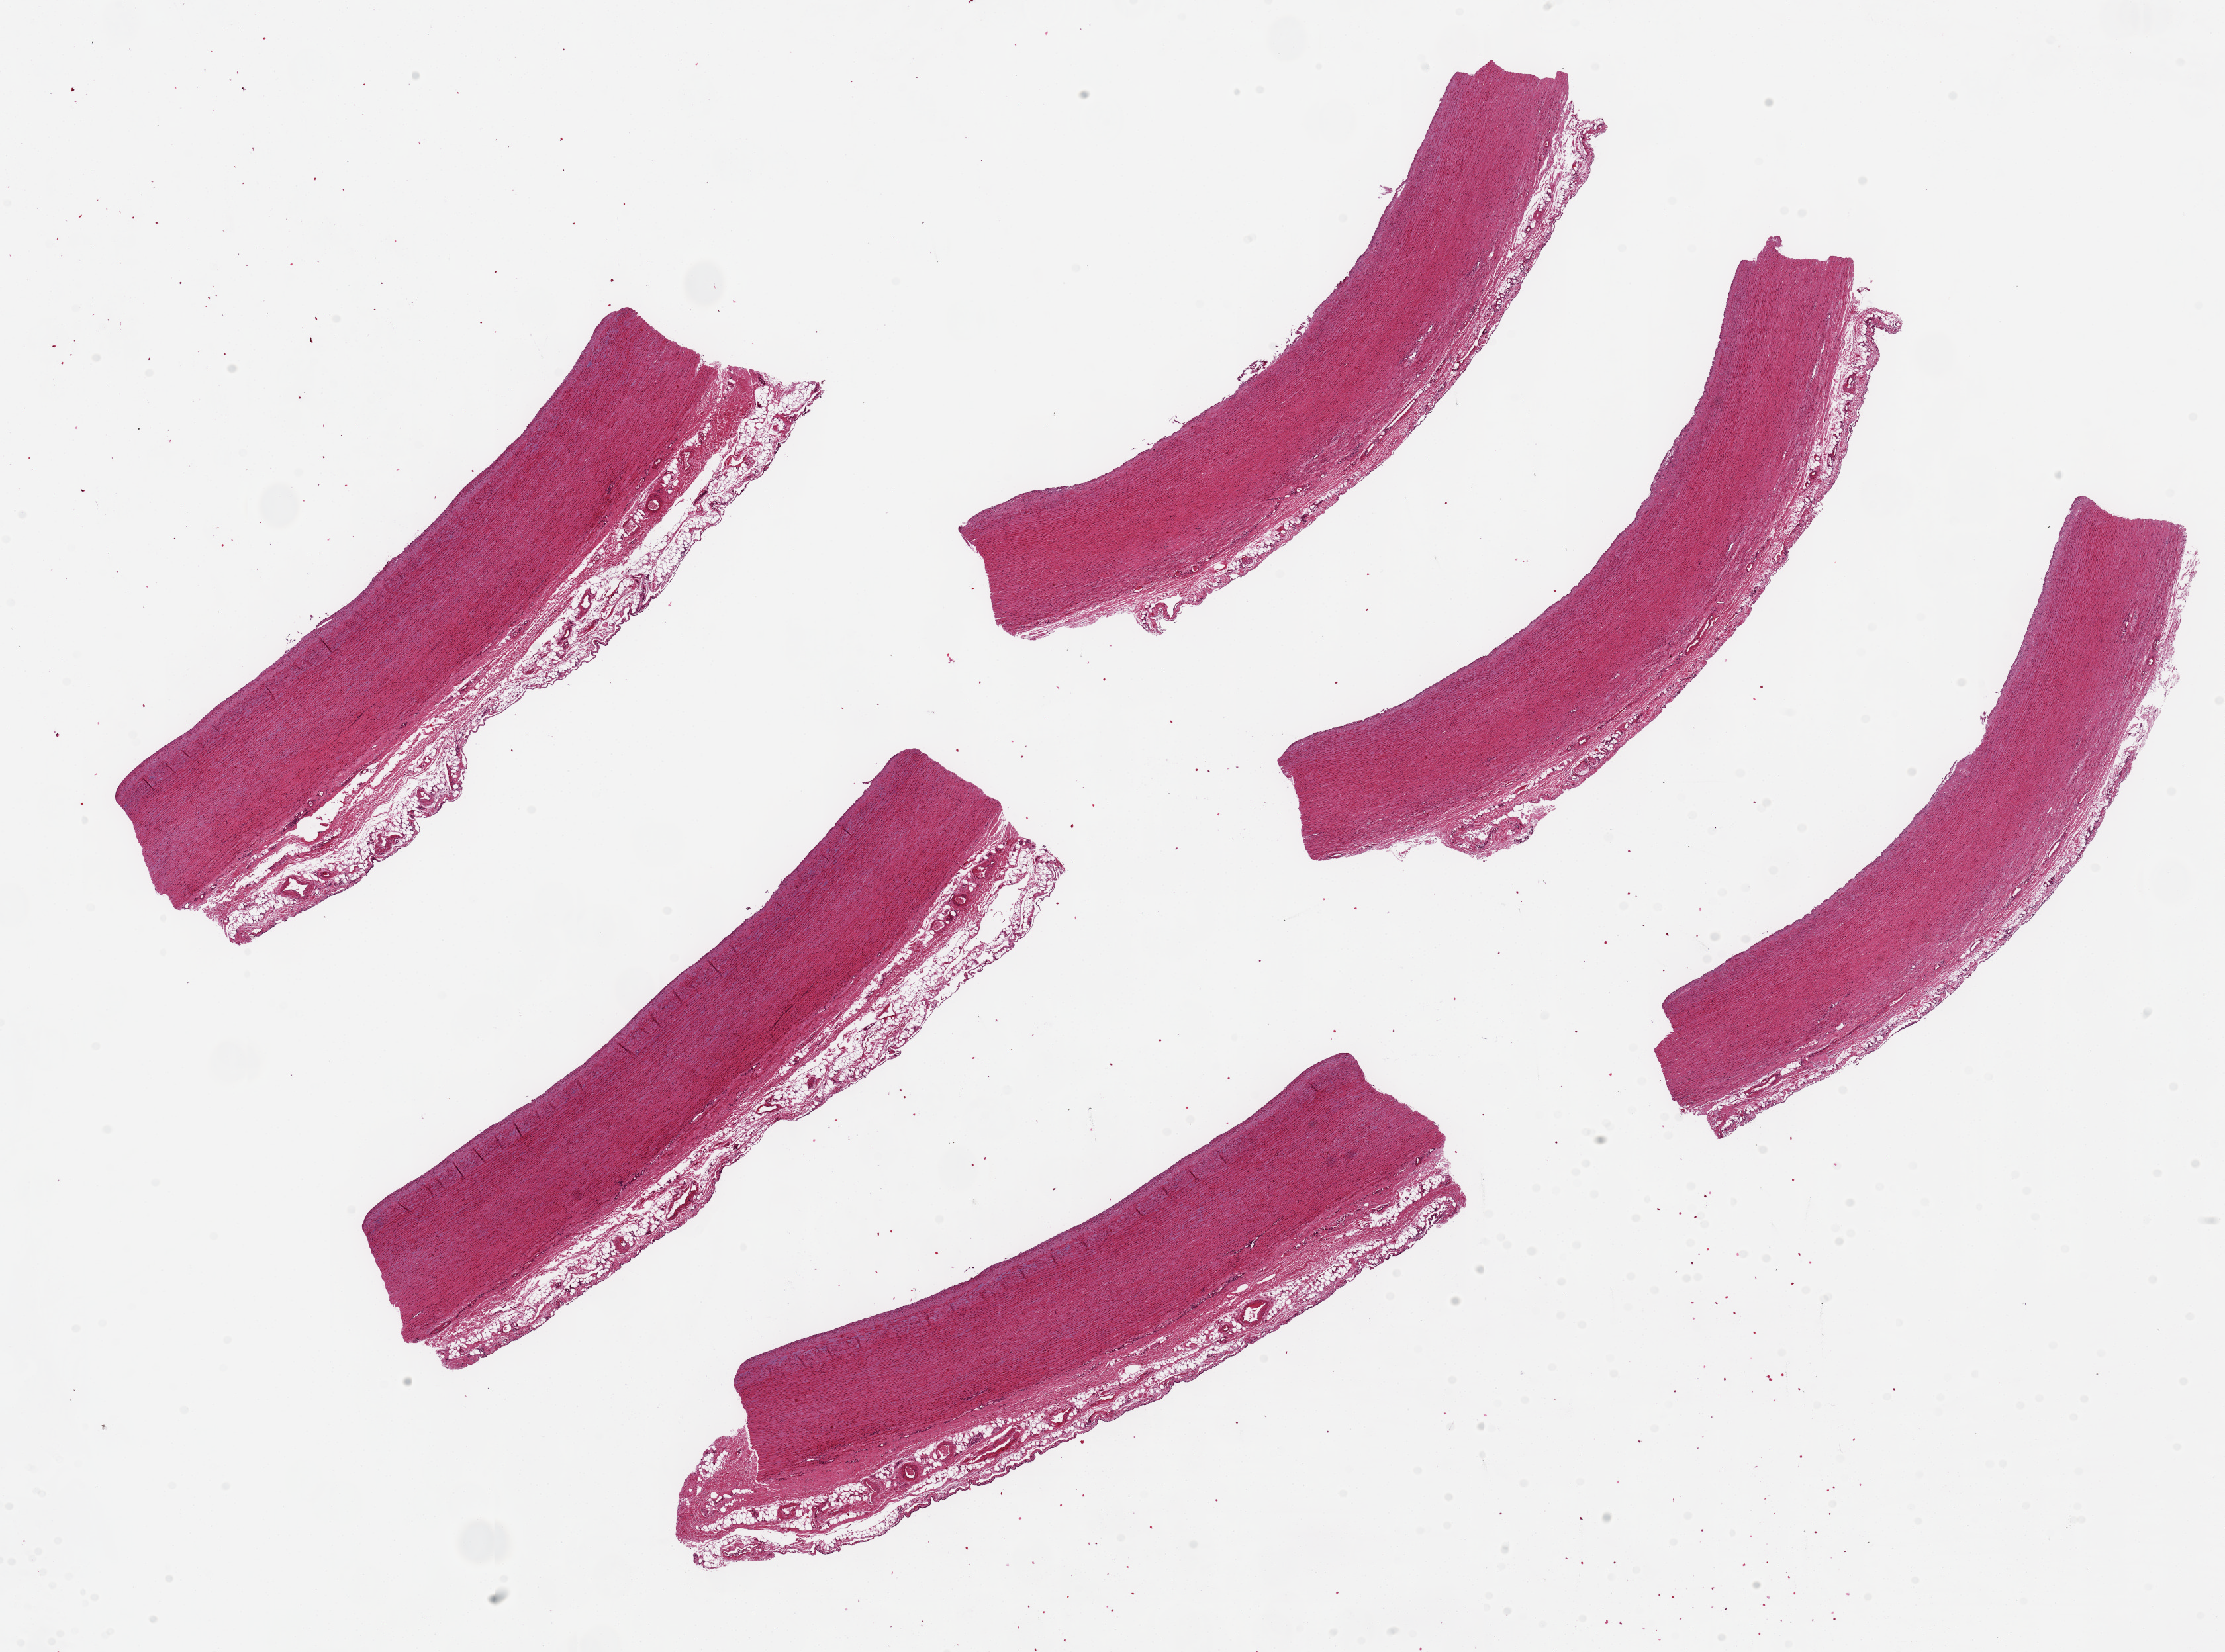
Whole-slide image, hematoxylin and eosin (H&E) stain, whole scanned area (about 26.6 x 19.7 mm, acquisition: 20x scan) shown as a low-resolution overview. PAXgene-fixed, paraffin-embedded tissue. Sampled site (target tissue): aorta. Tissue donor sample. Donor sex: female.
Reviewer comment on this tissue sample: 6 pieces, ~9x1.5 mm.